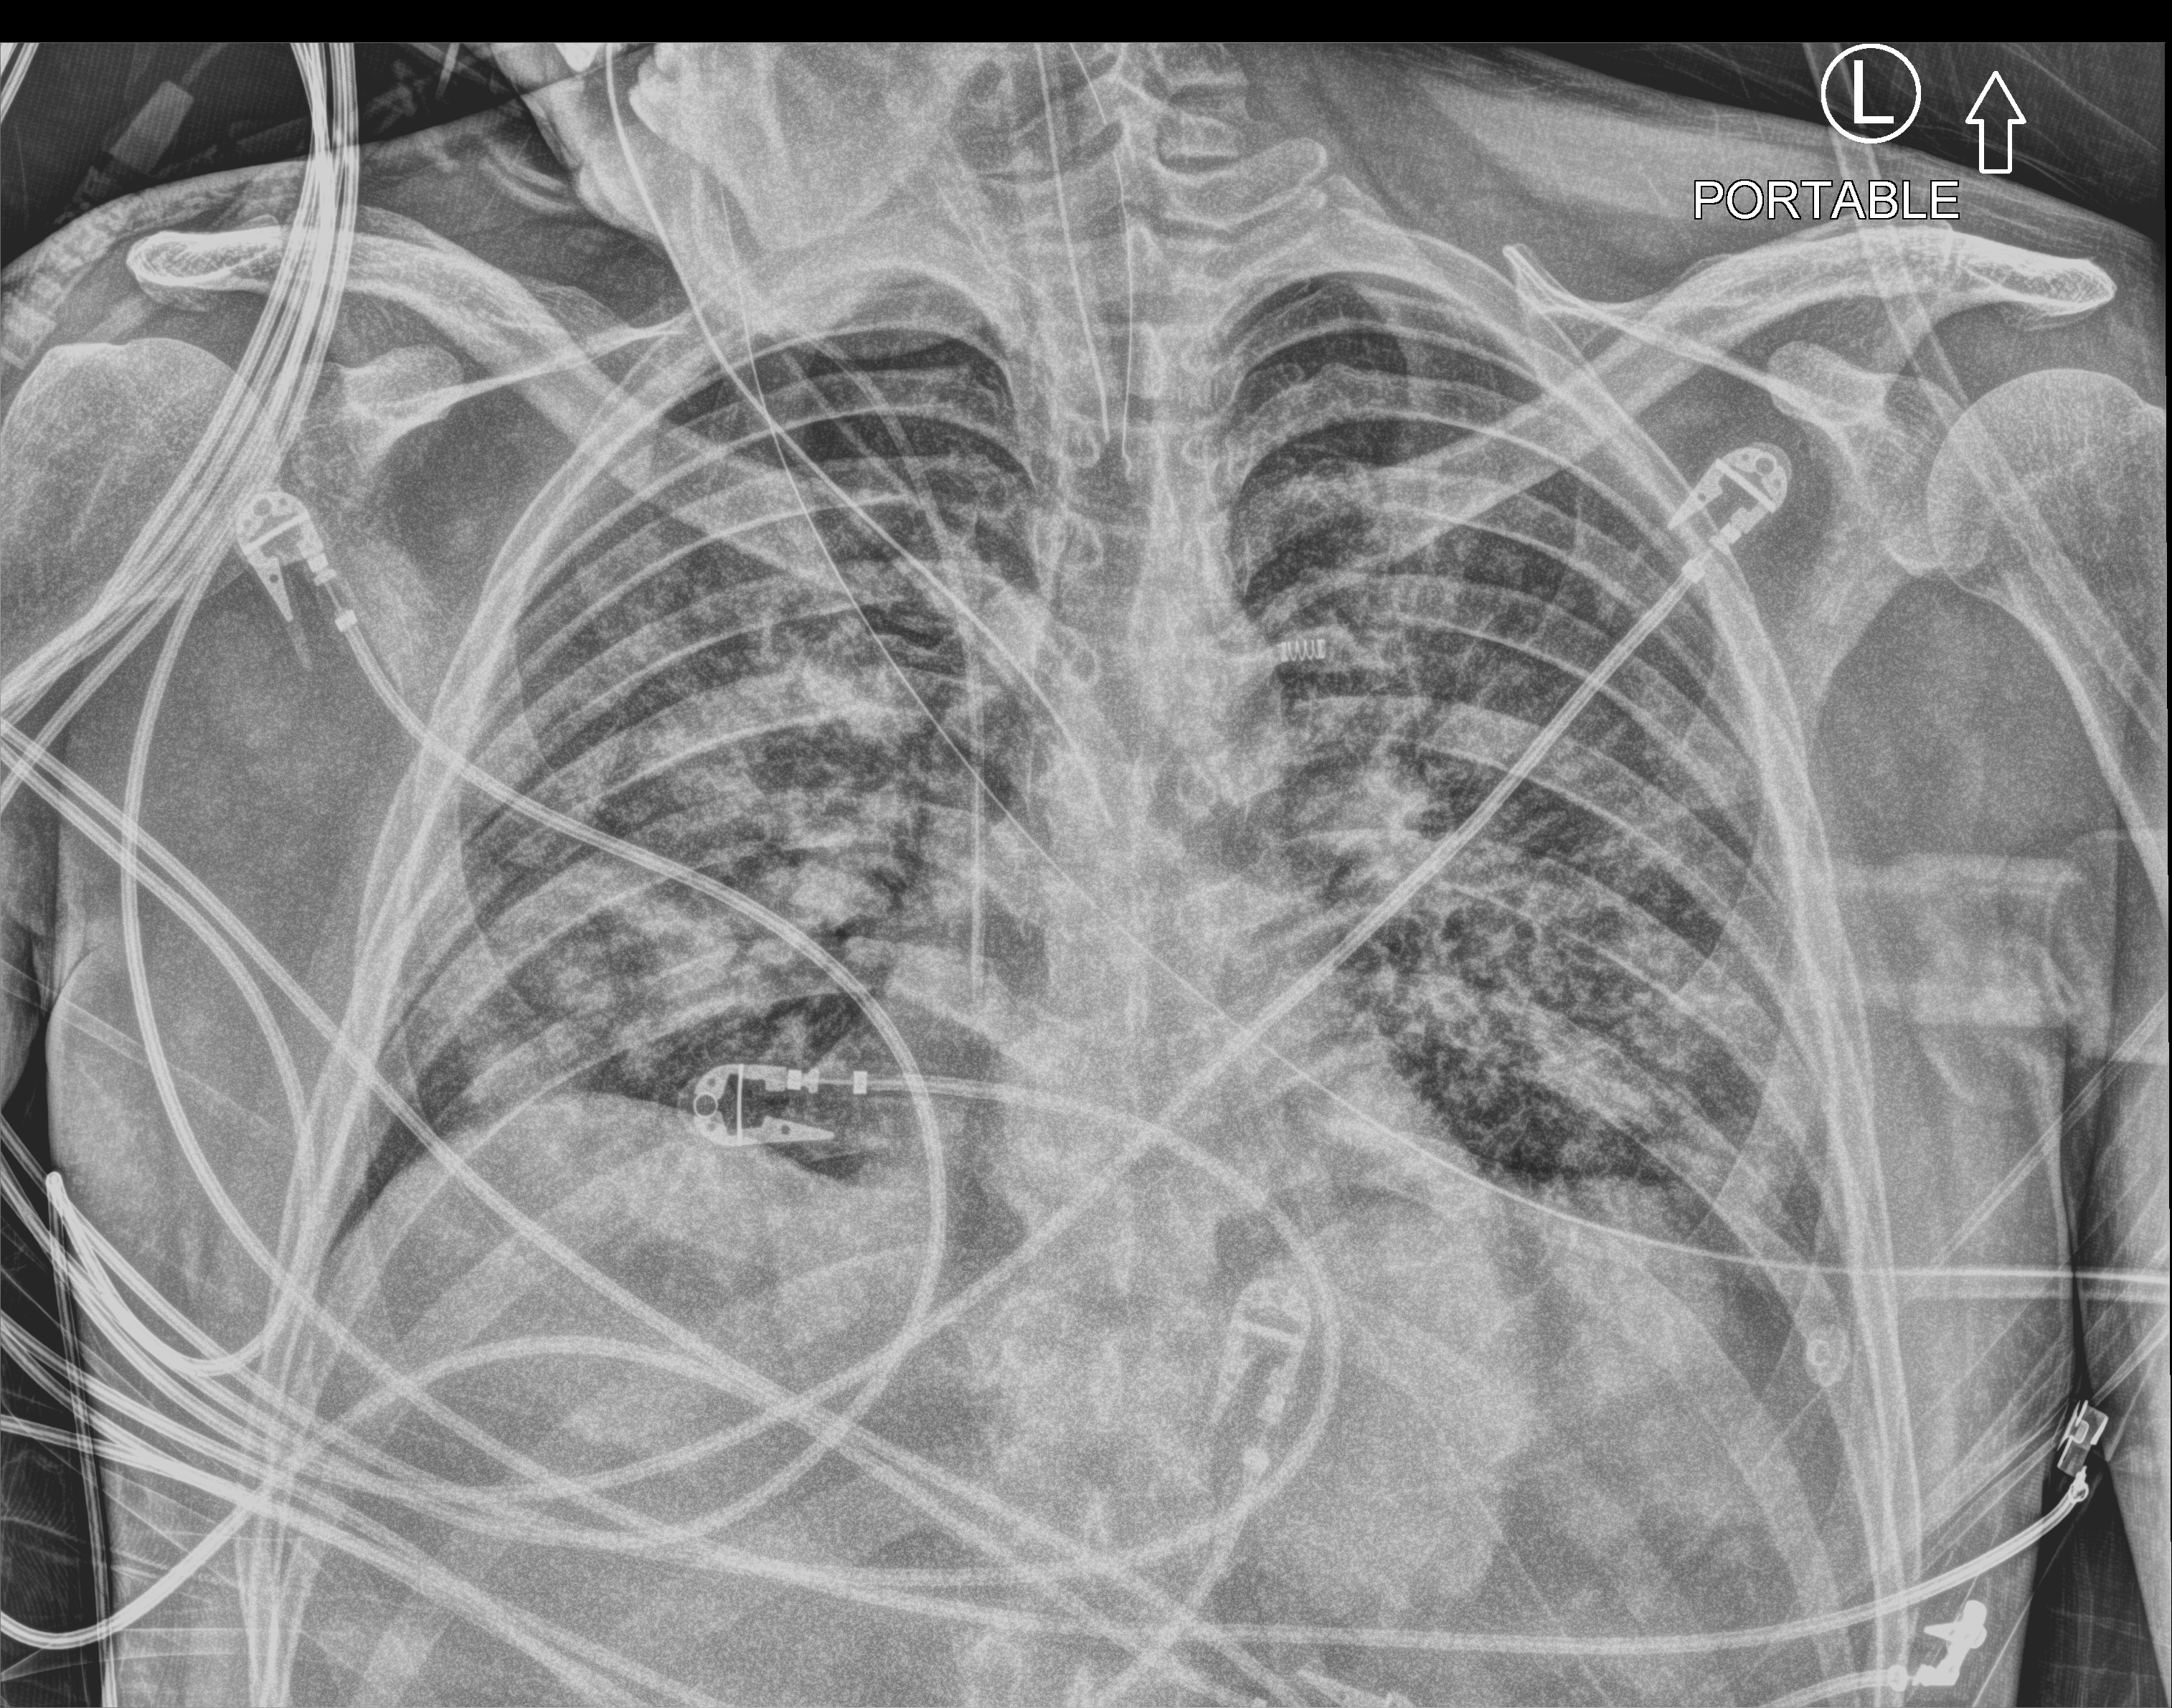
Portable chest radiograph; anteroposterior (AP) projection. Male patient hospitalised with COVID-19, age 18–59 years.
From the hospital-stay record, not from the radiograph (when in the stay this image was taken is not recorded): COPD (admission record): no; chronic kidney disease (admission record): no; admitted to intensive care during this hospital stay: yes.